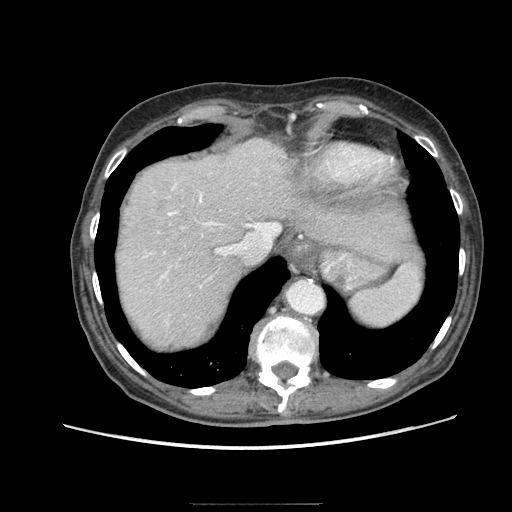
Contrast-enhanced abdominal CT (liver protocol), one axial slice; slice 69 of 83 in the series (ordered by position); reconstruction kernel STANDARD; soft-tissue window (W 400 / L 40 HU); 512 × 512 image matrix, field of view 360 × 360 mm. From the clinical record (not read from this slice): diagnosis: hepatocellular carcinoma (patient treated with transarterial chemoembolisation; whether this scan precedes or follows treatment is not stated here); TNM stage (as recorded): Stage-I.
Annotated regions visible in this slice (semi-automatic segmentation, software-assisted and operator-edited):
- abdominal aorta: bounding box <286,280,325,314> (left, top, right, bottom; pixels)
- liver parenchyma outside the tumour (the mass and vessels are separate outlines, so this box may not span the whole liver): <118,138,361,346>
- liver vessels: <145,185,251,287>